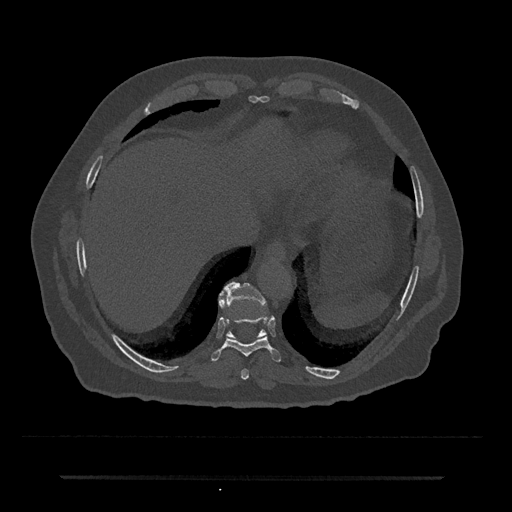
CT including the spine, one axial slice. Slice 268 of 797 in the series (ordered by position). Reconstruction kernel Br40s/3. 120 kVp. Bone window (W 1800 / L 400 HU). 0.5 mm slice thickness. 512 × 512 image matrix, field of view 437 × 437 mm. Patient: male, 69 years. From the clinical record (not read from this slice): primary cancer: prostate.
Annotated regions visible in this slice (semi-automatic segmentation, software-assisted and operator-edited):
- T10 vertebra: bounding box [x1, y1, x2, y2] px = [219, 282, 266, 339]
- T8 vertebra: [241, 369, 249, 380]
- T9 vertebra: [211, 291, 281, 362]